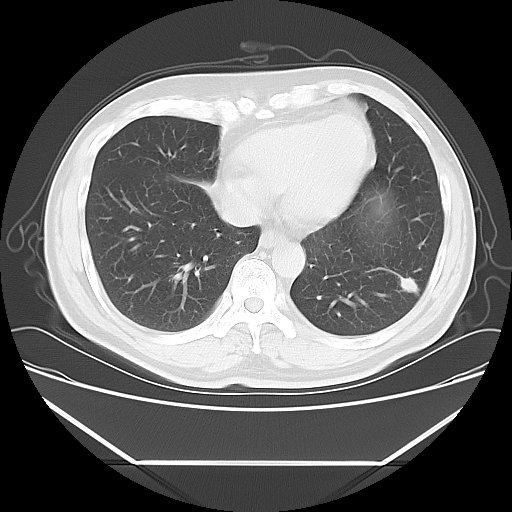
Chest CT, one axial slice. Position 19 of 57 along the scan axis. Reconstruction kernel LUNG. Lung window (W 1500 / L -600 HU). 5 mm slice thickness. 512 × 512 image matrix, field of view 384 × 384 mm. Patient: male, 53 years. Case-level facts recorded for this patient, not image findings: clinical TNM (as recorded): T1c N0 M0.
Annotated regions visible in this slice (rectangle marked by the reading radiologist):
- lung tumour (recorded histology: adenocarcinoma): bounding box [x1, y1, x2, y2] px = [384, 263, 423, 300]